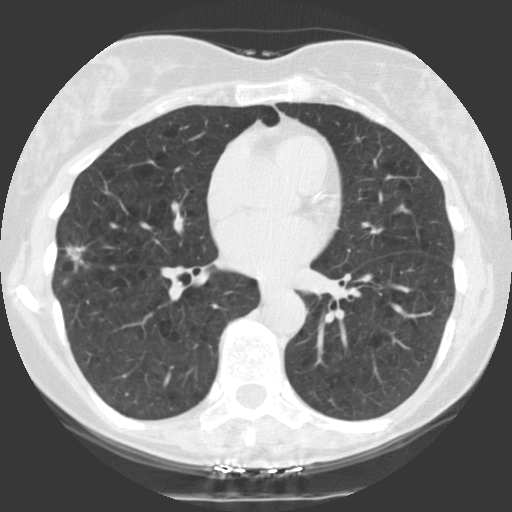
Low-dose screening chest CT, one axial slice. Position 58 of 123 along the scan axis. Reconstruction kernel STANDARD. 140 kVp. Lung window (W 1500 / L -600 HU). 2.5 mm slice thickness. 512 × 512 image matrix.
Outlined on this slice (manually delineated by an expert):
- lesion 1 (tumor, middle lobe of right lung): bounding box (x1, y1, x2, y2) in pixels: (66, 246, 85, 270)